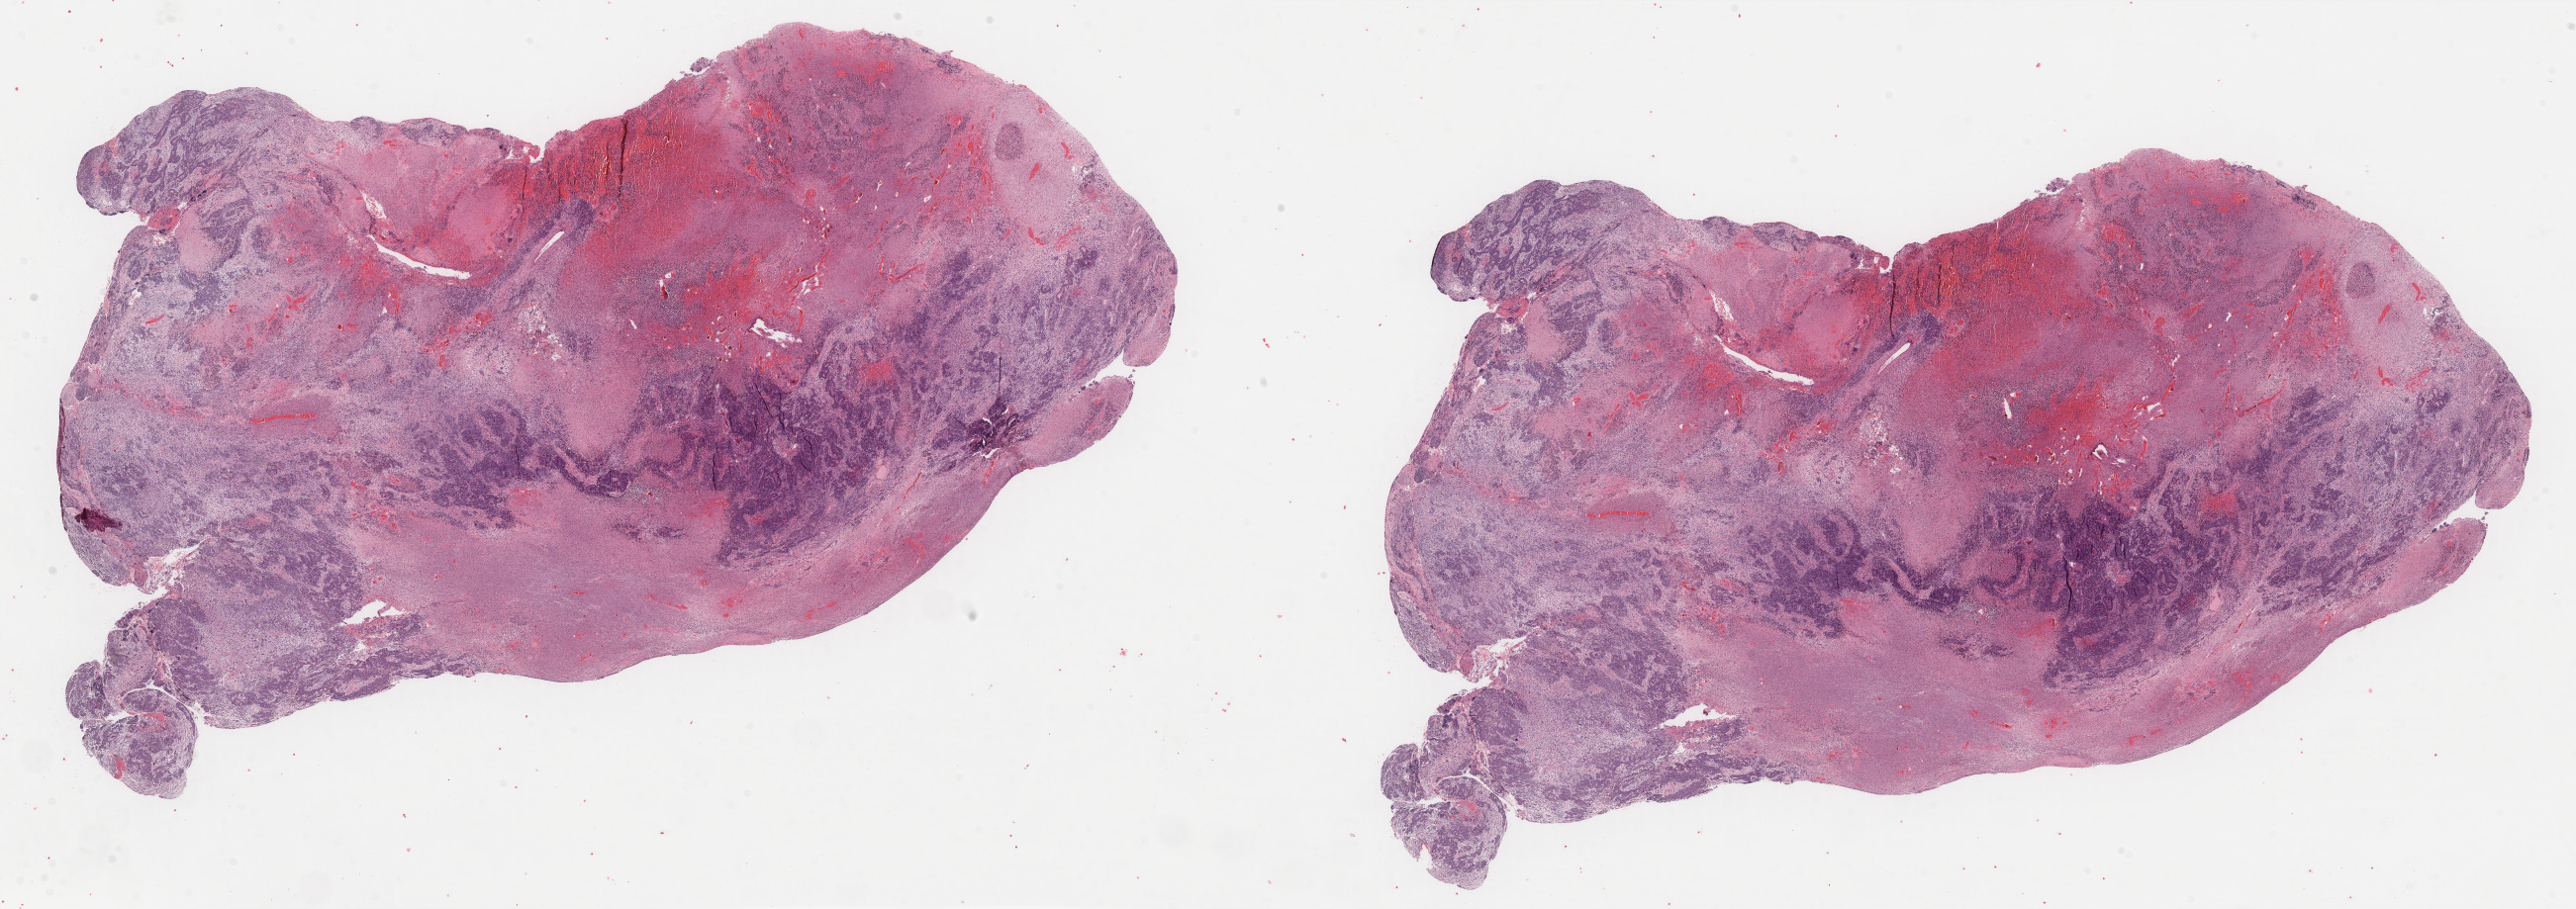
H&E whole-slide image, whole scanned area (about 41.2 x 14.5 mm, slide scanned at 40x) shown as a low-resolution overview; formalin-fixed paraffin-embedded (FFPE) diagnostic section; sample: primary tumour, uterus. Female, age 66 years at initial diagnosis.
Pathologic diagnosis: Carcinosarcoma, NOS (isthmus uteri).